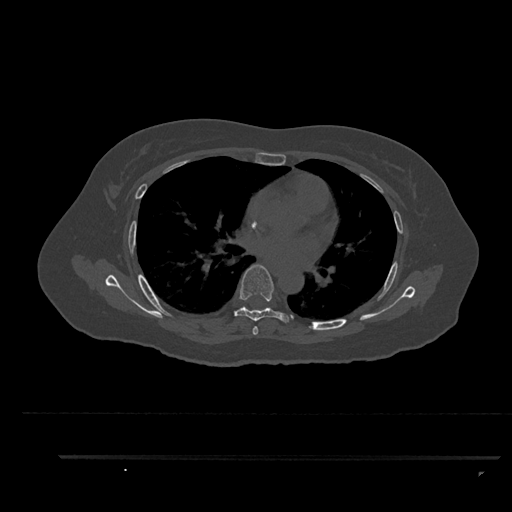
CT including the spine, one axial slice. Position 559 of 797 along the scan axis. Bone window (W 1800 / L 400 HU). 512 × 512 image matrix. Patient: female, 44 years. Case-level facts recorded for this patient, not image findings: primary cancer: renal; vertebrae with lytic lesions (as recorded): L1.
Outlined on this slice (semi-automatically segmented with operator editing):
- T5 vertebra: box from (x=253, y=326) to (x=258, y=335) px
- T6 vertebra: (x=234, y=264)–(x=292, y=335)